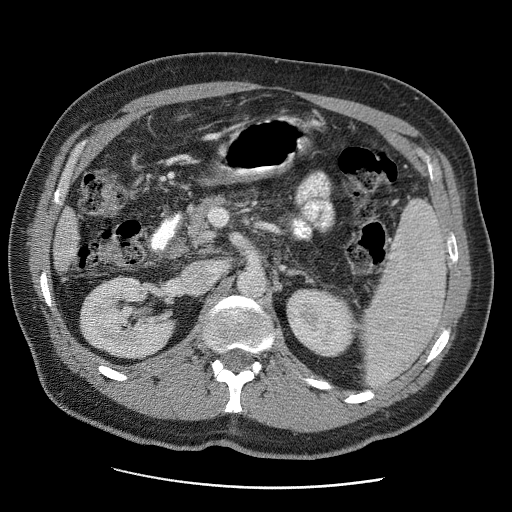
Contrast-enhanced abdominal CT (liver protocol), one axial slice. Reconstruction kernel STANDARD. 120 kVp. Soft-tissue window (W 400 / L 40 HU). 2.5 mm slice thickness. 512 × 512 image matrix, field of view 380 × 380 mm. From the clinical record (not read from this slice): diagnosis: hepatocellular carcinoma (patient treated with transarterial chemoembolisation; whether this scan precedes or follows treatment is not stated here); TNM stage (as recorded): Stage-IIIA; Child-Pugh class: A; tumour differentiation: moderately differentiated; tumour nodularity: multinodular.
Outlined on this slice (semi-automatic segmentation, software-assisted and operator-edited):
- liver parenchyma outside the tumour (the mass and vessels are separate outlines, so this box may not span the whole liver): box from (x=52, y=207) to (x=78, y=270) px